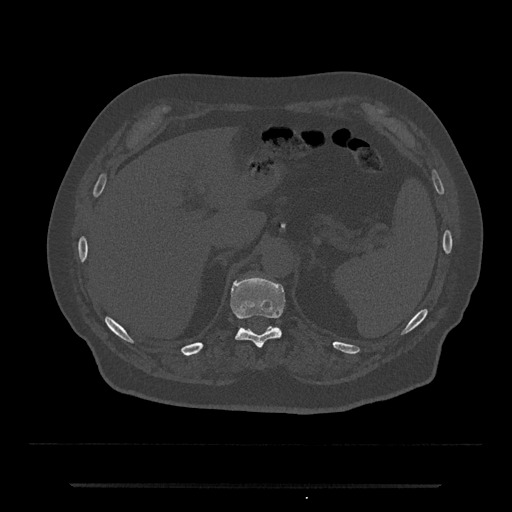
CT including the spine, one axial slice; slice 645 of 797 in the series (ordered by position); 120 kVp; bone window (W 1800 / L 400 HU); 0.5 mm slice thickness; 512 × 512 image matrix, field of view 434 × 434 mm. Male patient, age 80 years. Case-level facts recorded for this patient, not image findings: primary cancer: prostate.
Outlined on this slice (semi-automatic segmentation, software-assisted and operator-edited):
- T11 vertebra: bounding box <230,278,285,348> (left, top, right, bottom; pixels)